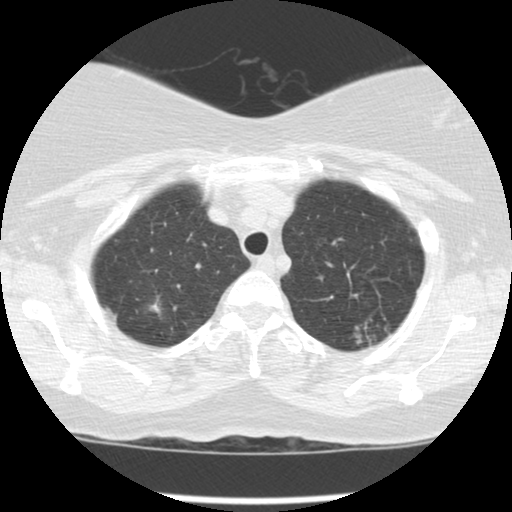
Low-dose screening chest CT, axial slice, third annual screen, lung window (W 1500 / L -600 HU), 2.5 mm slice thickness, 512 × 512 image matrix, field of view 310 × 310 mm. Female, age 56 years at enrolment. Current smoker at enrolment.
Lesion marked by an expert reader, bounding box (x1, y1, x2, y2) in pixels: (329, 299, 404, 355). The screening reader recorded 4 non-calcified nodules or masses ≥4 mm on this exam; which of them this box marks is not recorded.